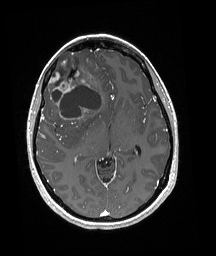
Brain MRI from a brain-tumour surgery series, one axial slice. Position 105 of 192 along the scan axis. T1-weighted post-contrast. 1 mm slice thickness. 216 × 256 image matrix. Case-level facts recorded for this patient, not image findings: histopathology: Oligodendroglioma; WHO grade: 3; IDH mutation: yes.
Annotated regions visible in this slice (outlined manually by an expert reader):
- tumour: bounding box (x1, y1, x2, y2) in pixels: (49, 52, 102, 119)